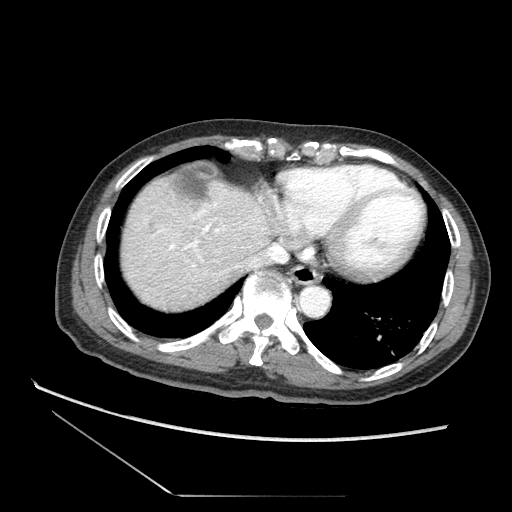
Contrast-enhanced abdominal CT (liver protocol), one axial slice. Slice 67 of 73 in the series (ordered by position). Reconstruction kernel STANDARD. Soft-tissue window (W 400 / L 40 HU). 512 × 512 image matrix, field of view 360 × 360 mm. Case-level facts recorded for this patient, not image findings: diagnosis: hepatocellular carcinoma (patient treated with transarterial chemoembolisation; whether this scan precedes or follows treatment is not stated here); TNM stage (as recorded): Stage-II; Child-Pugh class: A.
Annotated regions visible in this slice (semi-automatic segmentation, software-assisted and operator-edited):
- abdominal aorta: box from (x=302, y=286) to (x=330, y=316) px
- liver parenchyma outside the tumour (the mass and vessels are separate outlines, so this box may not span the whole liver): (x=116, y=175)–(x=285, y=316)
- mass: (x=121, y=268)–(x=148, y=300)
- liver vessels: (x=195, y=240)–(x=283, y=247)